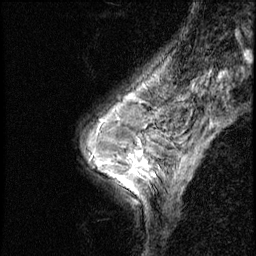
Breast MRI (dynamic contrast-enhanced), one sagittal slice; position 38 of 56 along the scan axis; dynamic contrast-enhanced series, image 2 of 3 at this slice position (ordered by acquisition); 1.5 T; TE 4.2 ms, TR 8.7 ms; 256 × 256 image matrix, field of view 180 × 180 mm. Female patient, age 50 years. From the clinical record (not read from this slice): setting: breast cancer imaged before/during neoadjuvant chemotherapy; receptor status: HR-positive, HER2-negative.
Outlined on this slice (semi-automatically segmented with operator editing):
- analysis volume of interest (the breast-tissue region the enhancement analysis was run in; not a lesion): bounding box <119,136,169,190> (left, top, right, bottom; pixels)
- tumour enhancement mask (voxels above the 140 % enhancement threshold inside the analysis volume of interest): <131,143,147,173>